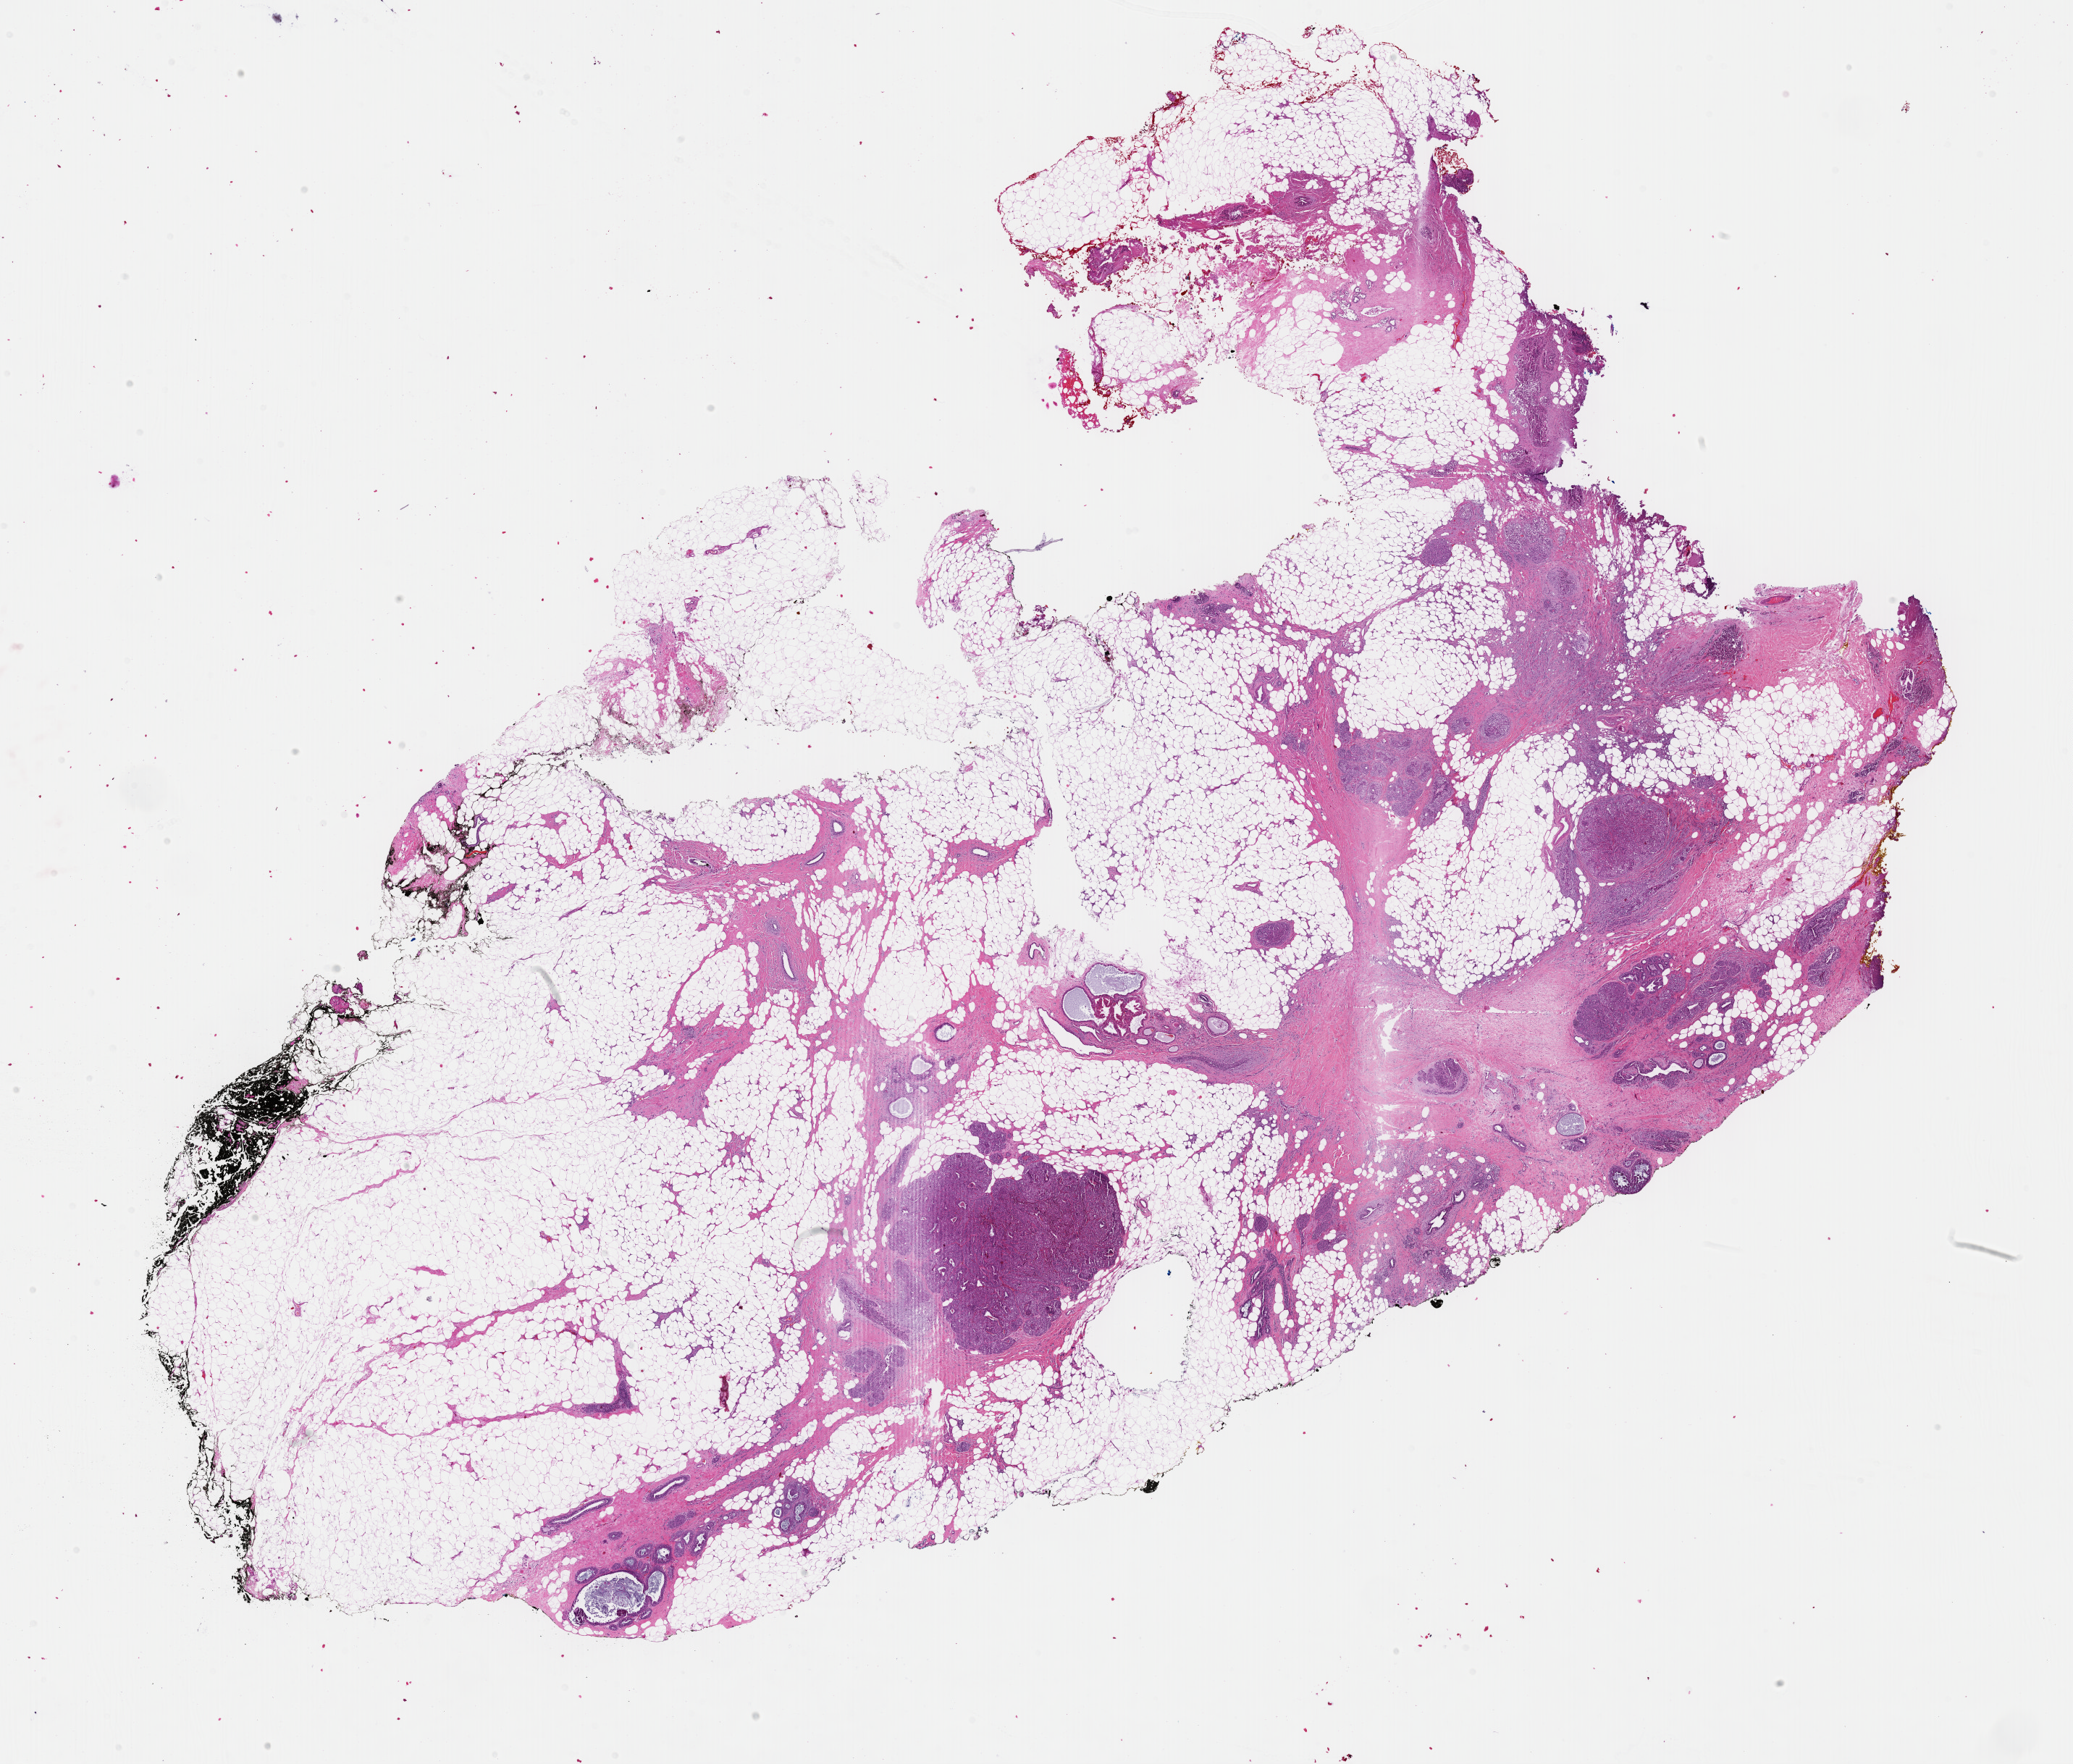
Whole-slide histology image, H&E, shown as a low-resolution overview of the whole scanned area (about 23.2 x 19.7 mm, from a 40x scan), formalin-fixed paraffin-embedded (FFPE) diagnostic section, primary tumour sample from the breast. Patient: female, age at initial diagnosis 66 years.
Pathologic diagnosis: Lobular carcinoma, NOS. AJCC pathologic stage: IIA.